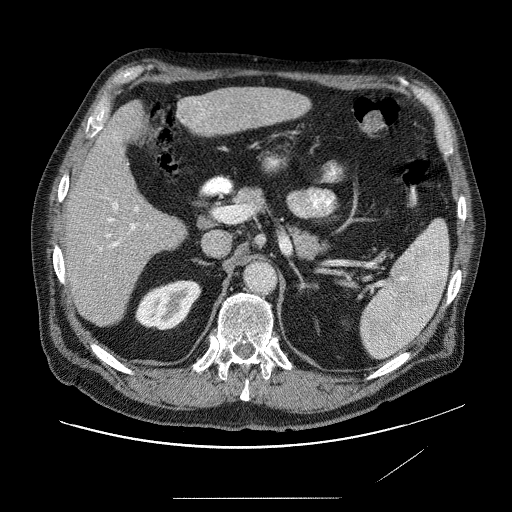
Contrast-enhanced abdominal CT (liver protocol), one axial slice. Slice 38 of 89 in the series (ordered by position). Reconstruction kernel STANDARD. 120 kVp. Soft-tissue window (W 400 / L 40 HU). 2.5 mm slice thickness. 512 × 512 image matrix, field of view 420 × 420 mm. From the clinical record (not read from this slice): diagnosis: hepatocellular carcinoma (patient treated with transarterial chemoembolisation; whether this scan precedes or follows treatment is not stated here); TNM stage (as recorded): Stage-IVA; Child-Pugh class: A.
Annotated regions visible in this slice (semi-automatic segmentation, software-assisted and operator-edited):
- liver parenchyma outside the tumour (the mass and vessels are separate outlines, so this box may not span the whole liver): box from (x=62, y=84) to (x=316, y=326) px
- mass: (x=181, y=96)–(x=210, y=128)
- liver vessels: (x=89, y=99)–(x=283, y=281)